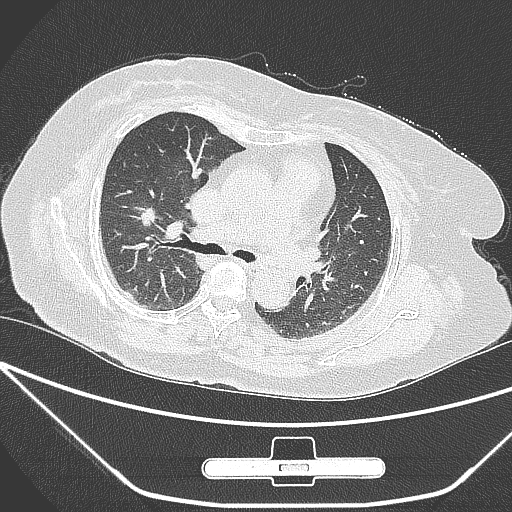
Chest CT, one axial slice. Position 165 of 245 along the scan axis. 120 kVp. Lung window (W 1500 / L -600 HU). 1 mm slice thickness. 512 × 512 image matrix. Patient: female, 65 years. Case-level facts recorded for this patient, not image findings: clinical TNM (as recorded): T1c N0 M0; histopathological grade: G3.
Structures marked on this image (rectangle marked by the reading radiologist):
- lung tumour (recorded histology: adenocarcinoma): box from (x=140, y=200) to (x=159, y=232) px